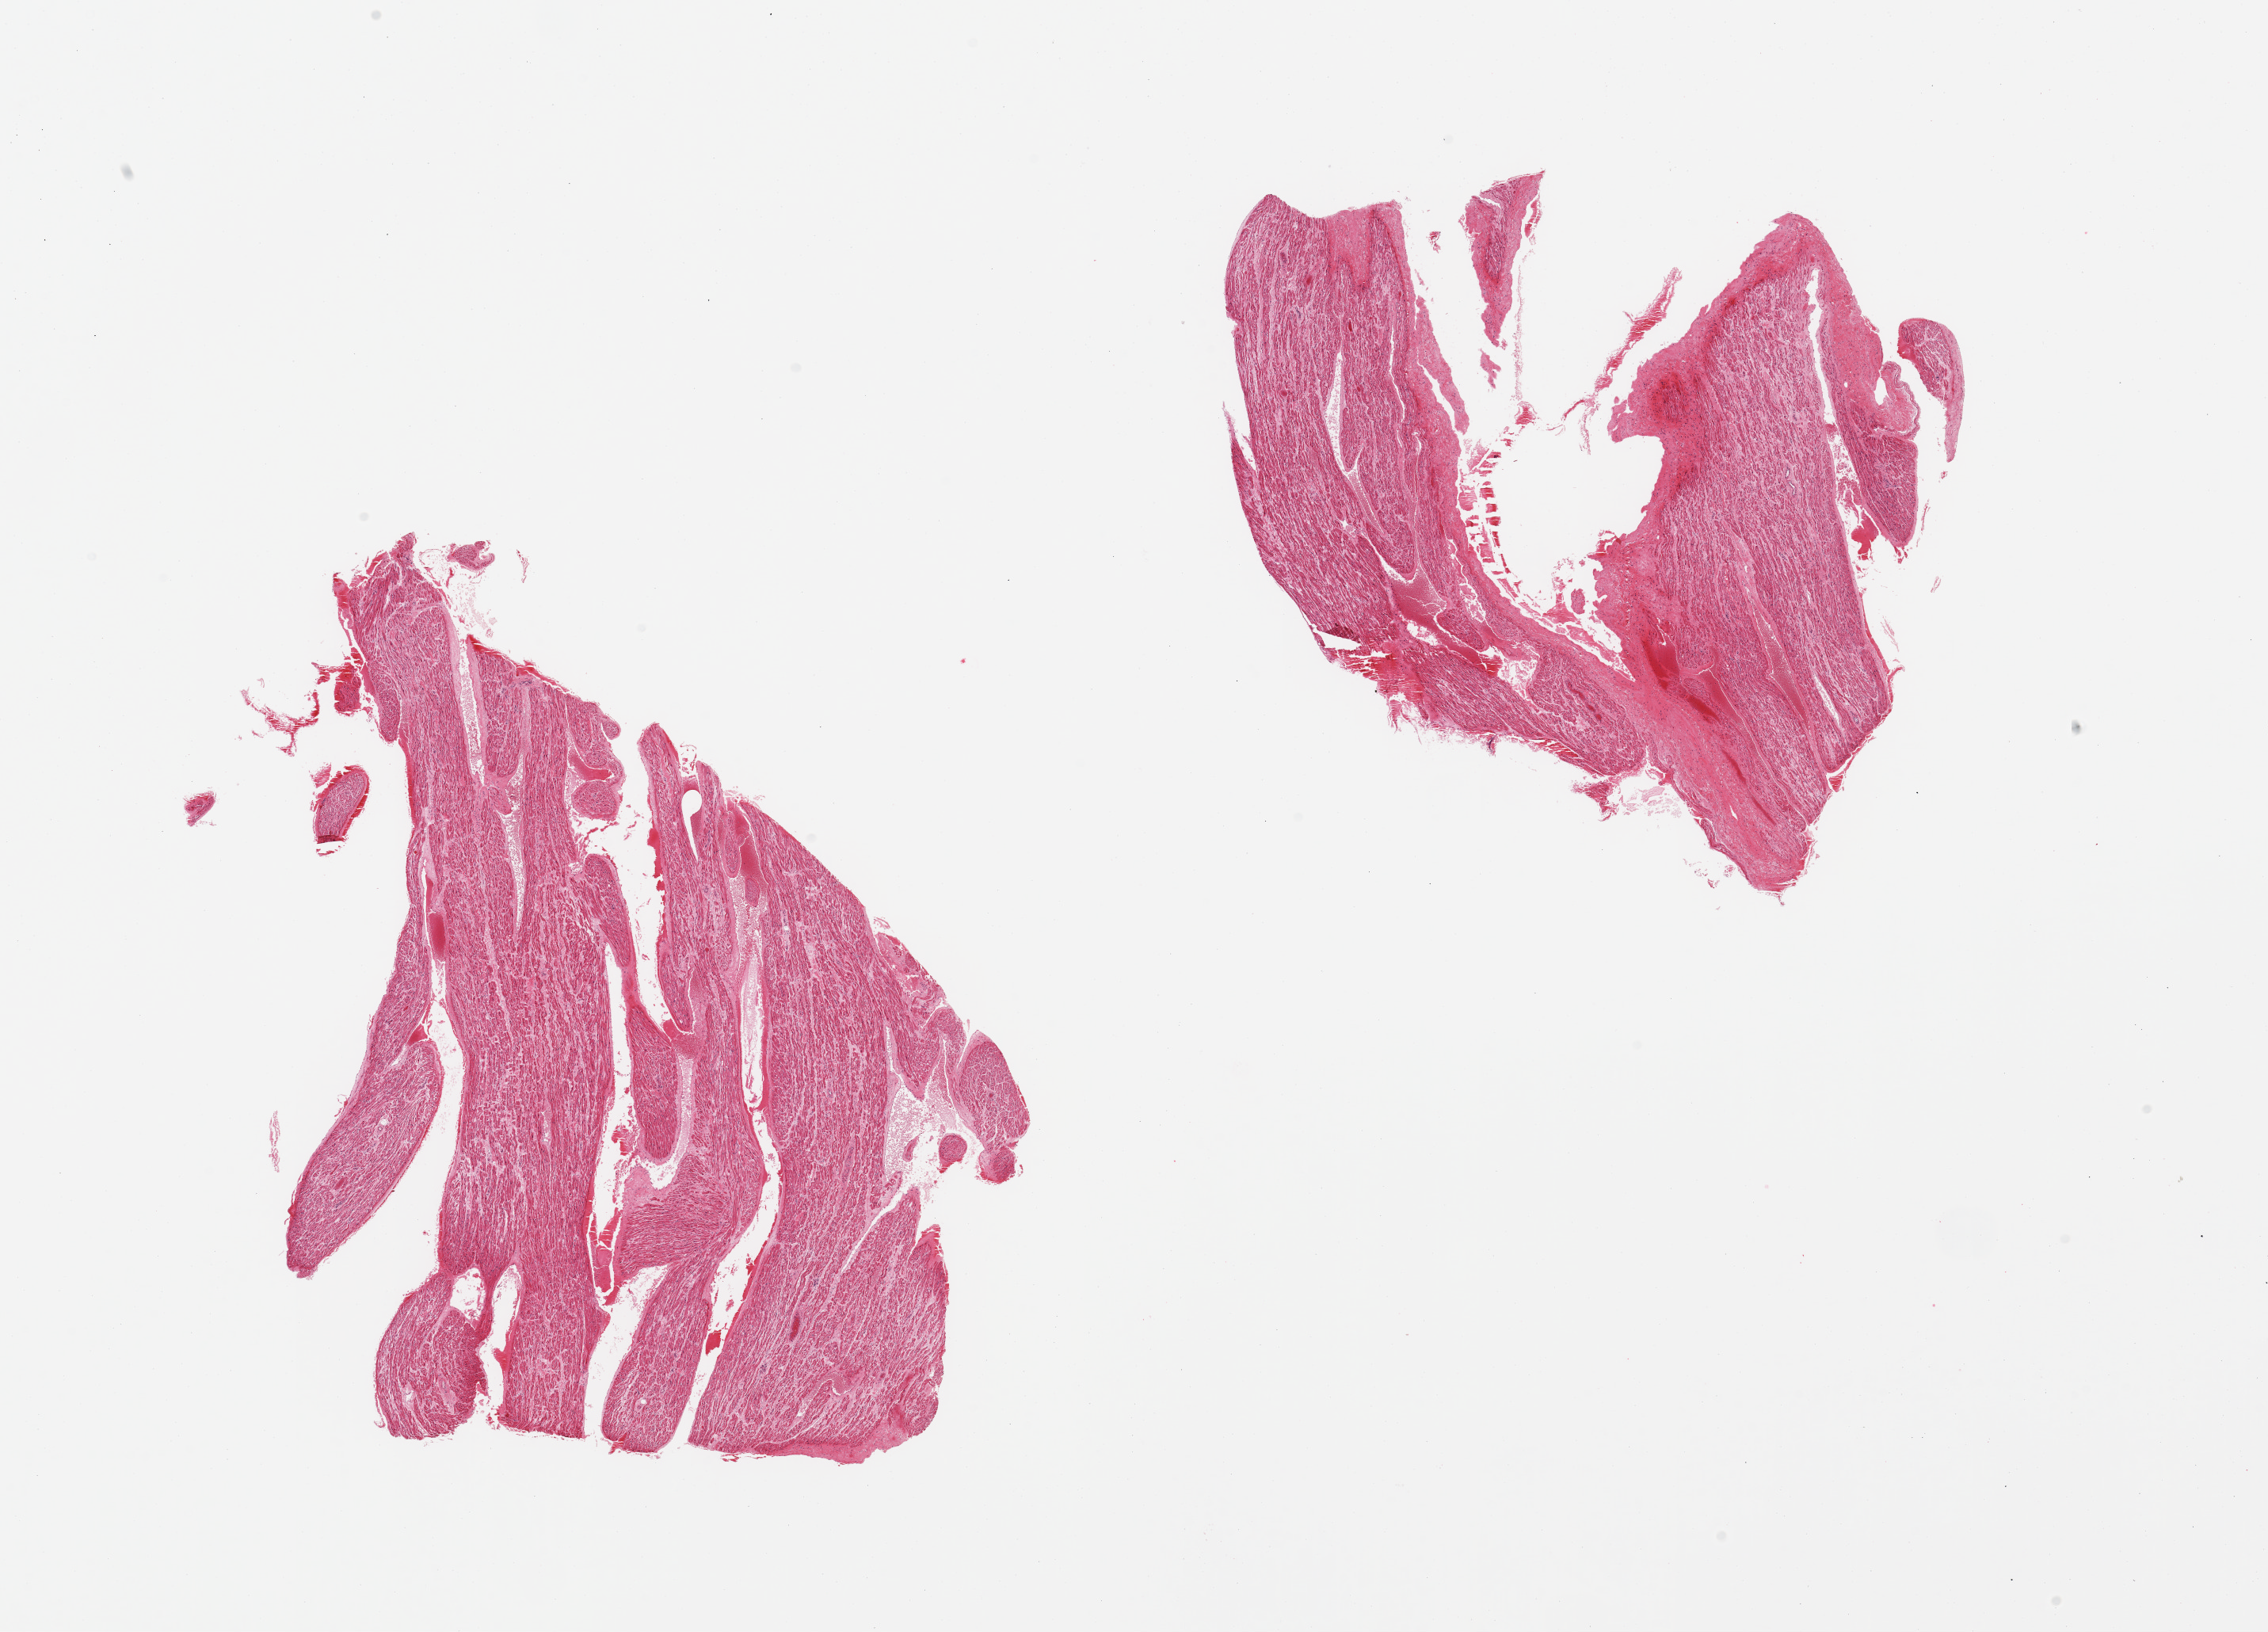
Hematoxylin and eosin (H&E) whole-slide image — low-resolution overview of the scanned area, about 22.6 x 16.3 mm (slide scanned at 20x); PAXgene-fixed paraffin-embedded (PFPE) section; sampled site (target tissue): auricular appendage; donor tissue sample. Donor sex: male.
- pathologist's review note for this sample: 2 pieces